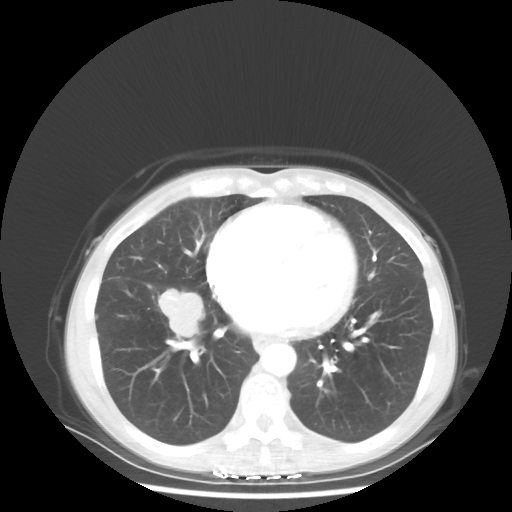
Chest CT, one axial slice. Slice 22 of 56 in the series (ordered by position). Reconstruction kernel STANDARD. 80 kVp. Lung window (W 1500 / L -600 HU). 512 × 512 image matrix, field of view 360 × 360 mm. Patient: female, 57 years. Case-level facts recorded for this patient, not image findings: clinical TNM (as recorded): T1c N3 M1a; histopathological grade: G3.
Annotated regions visible in this slice (bounding box drawn by a radiologist):
- lung tumour (recorded histology: adenocarcinoma): bounding box <156,280,206,343> (left, top, right, bottom; pixels)